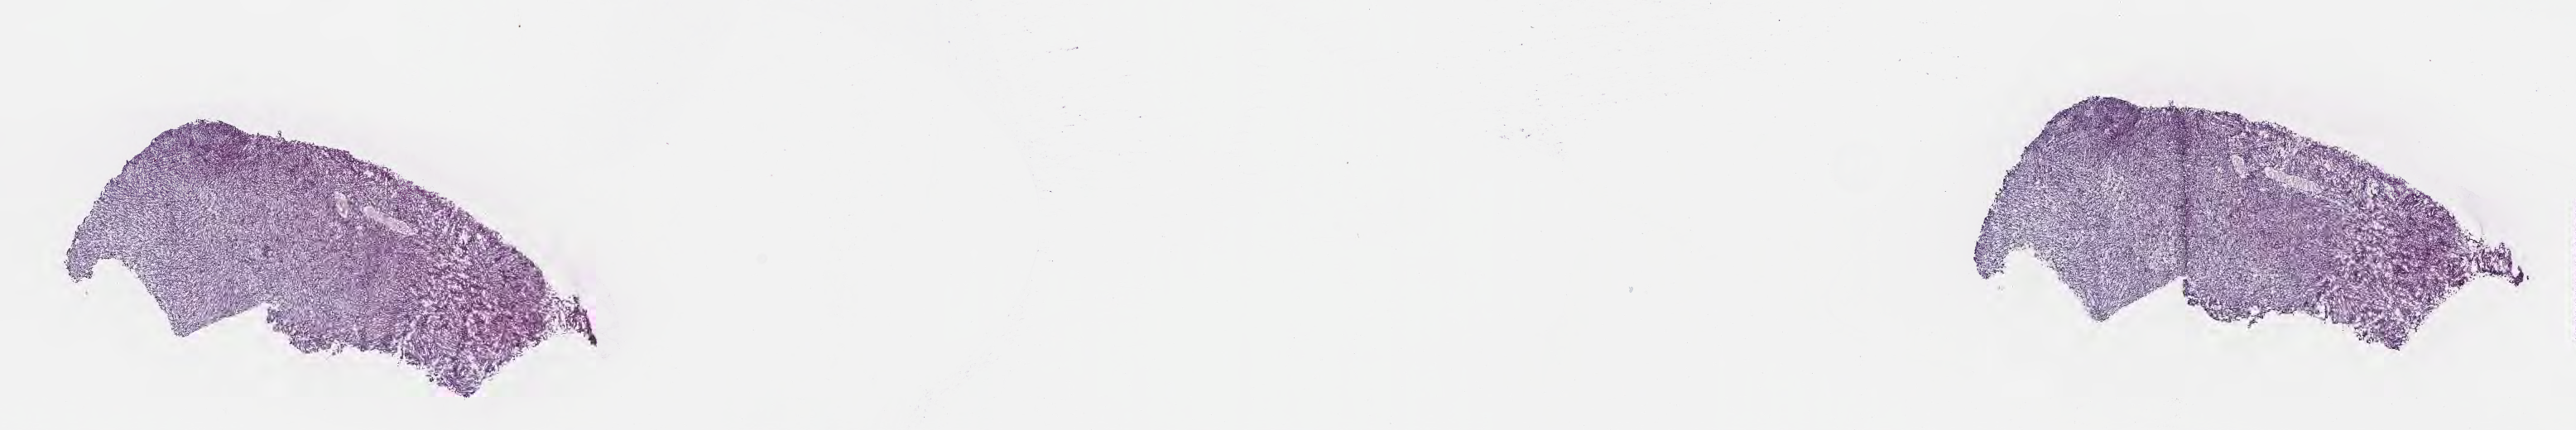
Whole-slide image, haematoxylin and eosin stain, a low-resolution overview of the entire scanned area, about 25.1 x 4.2 mm; frozen section (tissue freezing medium); primary tumor; site: brain. Male, age 37 years at initial diagnosis. Composition of this section per pathologist review: tumor cells 62%, tumor nuclei 82%, stromal cells 25%, necrosis 0%, normal cells 13%. Infiltration values recorded for this section: lymphocyte infiltration 0%, monocyte infiltration 0%, neutrophil infiltration 0%.
Section: bottom of the tissue portion. Histologic diagnosis: Glioblastoma, NOS.